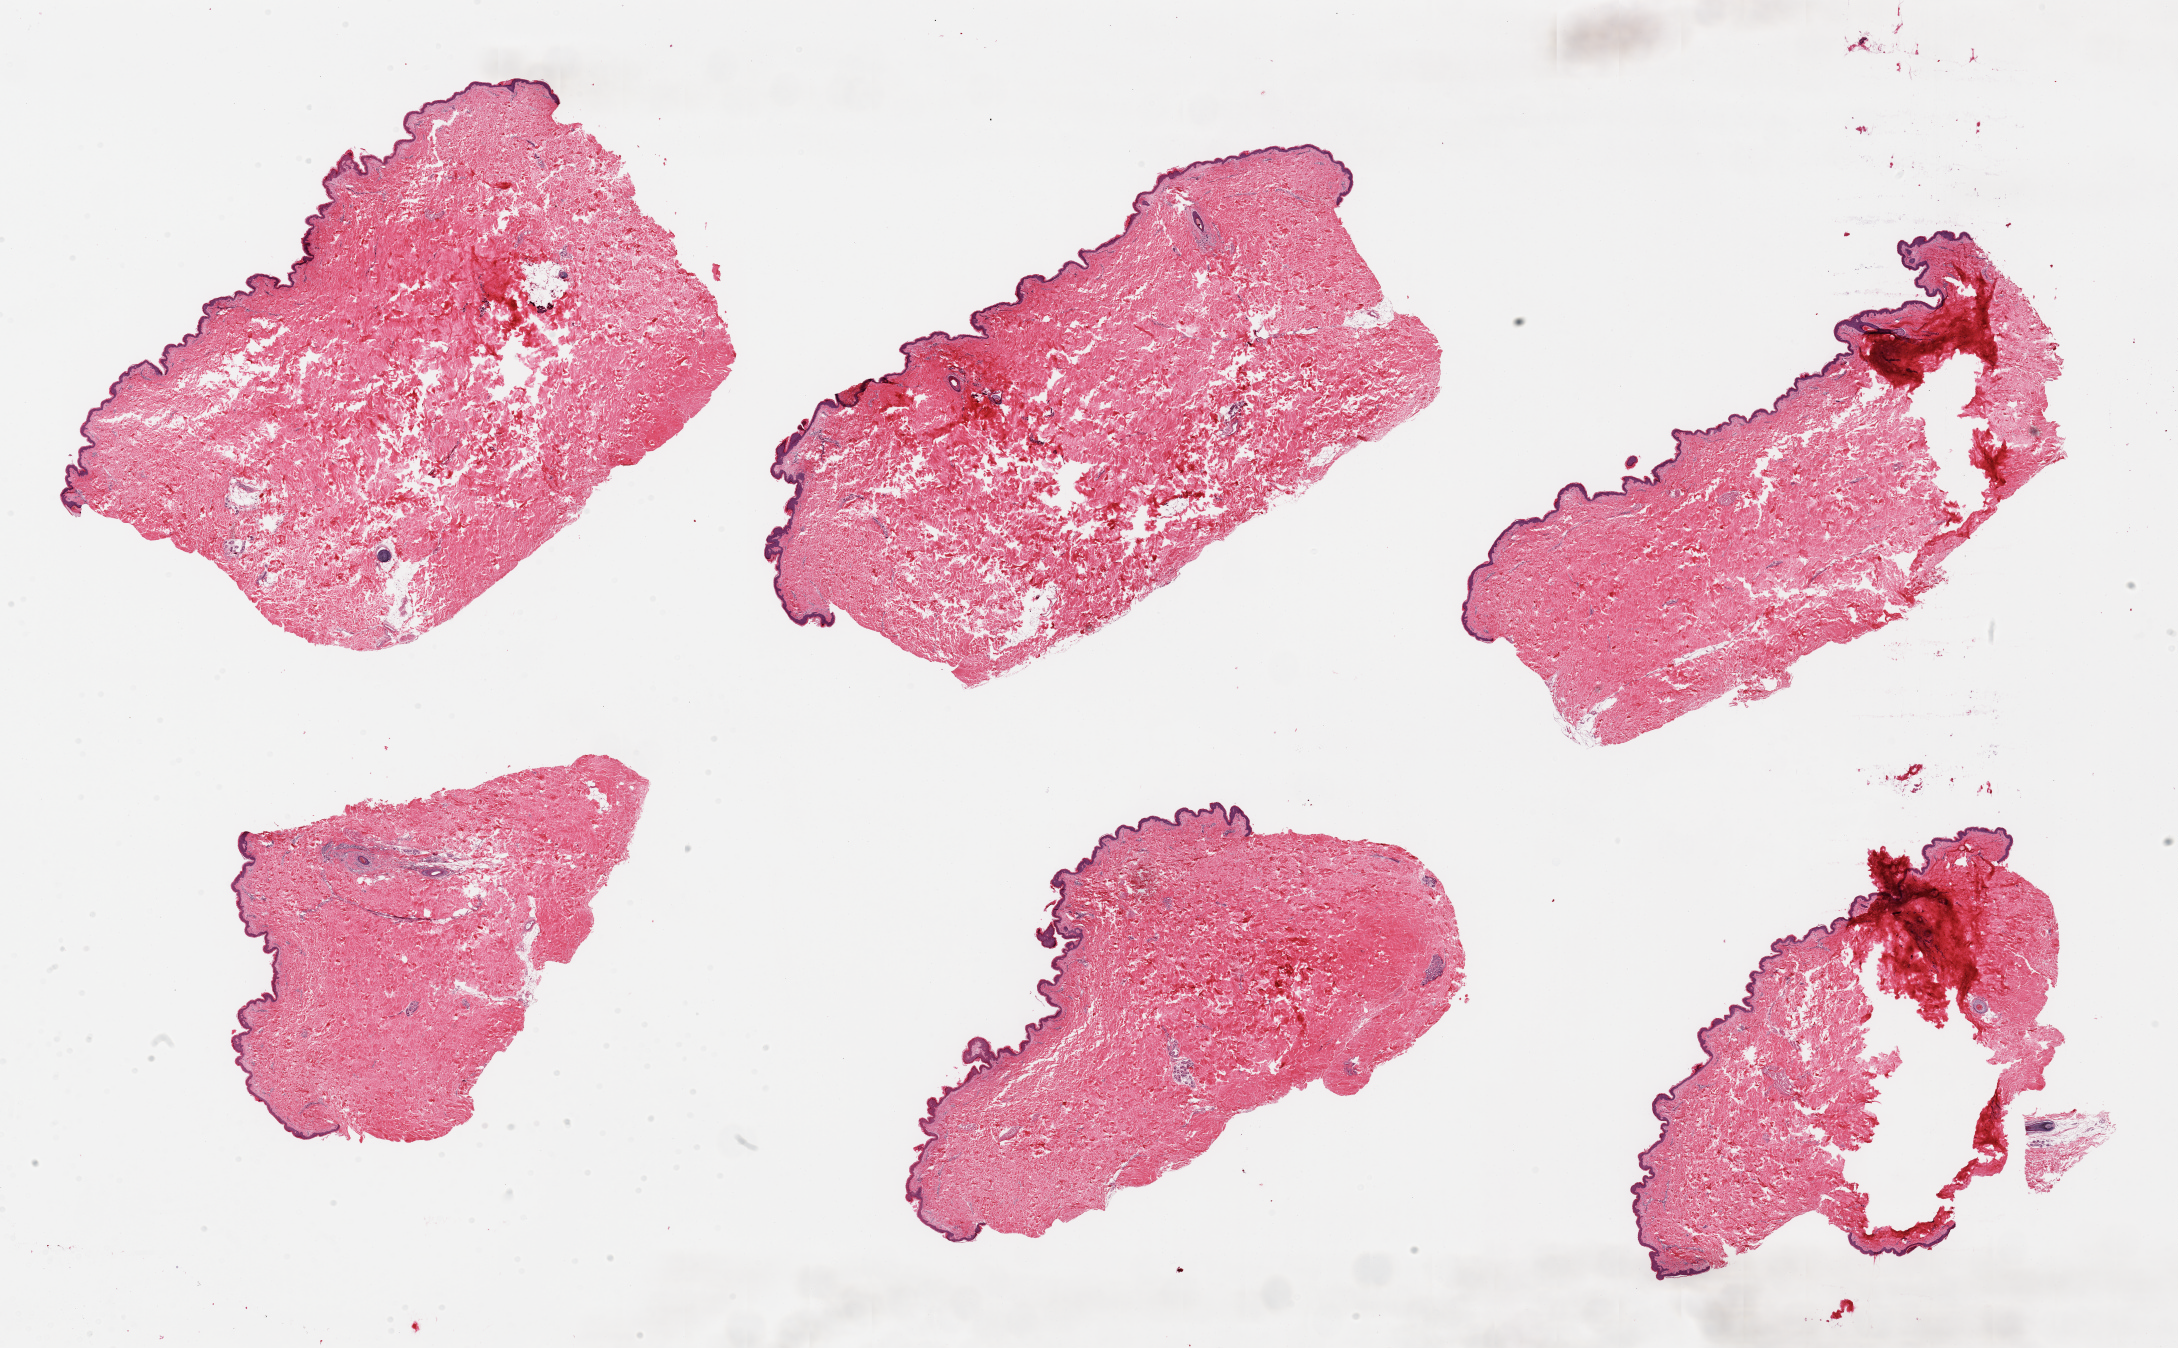
Digitized H&E-stained section, a low-resolution overview of the entire scanned area, about 34.5 x 21.3 mm (from a 20x scan); PAXgene-fixed paraffin-embedded (PFPE) section; sampled site (target tissue): skin of suprapubic region; donor tissue sample. Male donor.
Reviewer comment on this tissue sample: 6 pieces, no adherent dermal fat; squamous epithelium is ~50-60 microns.